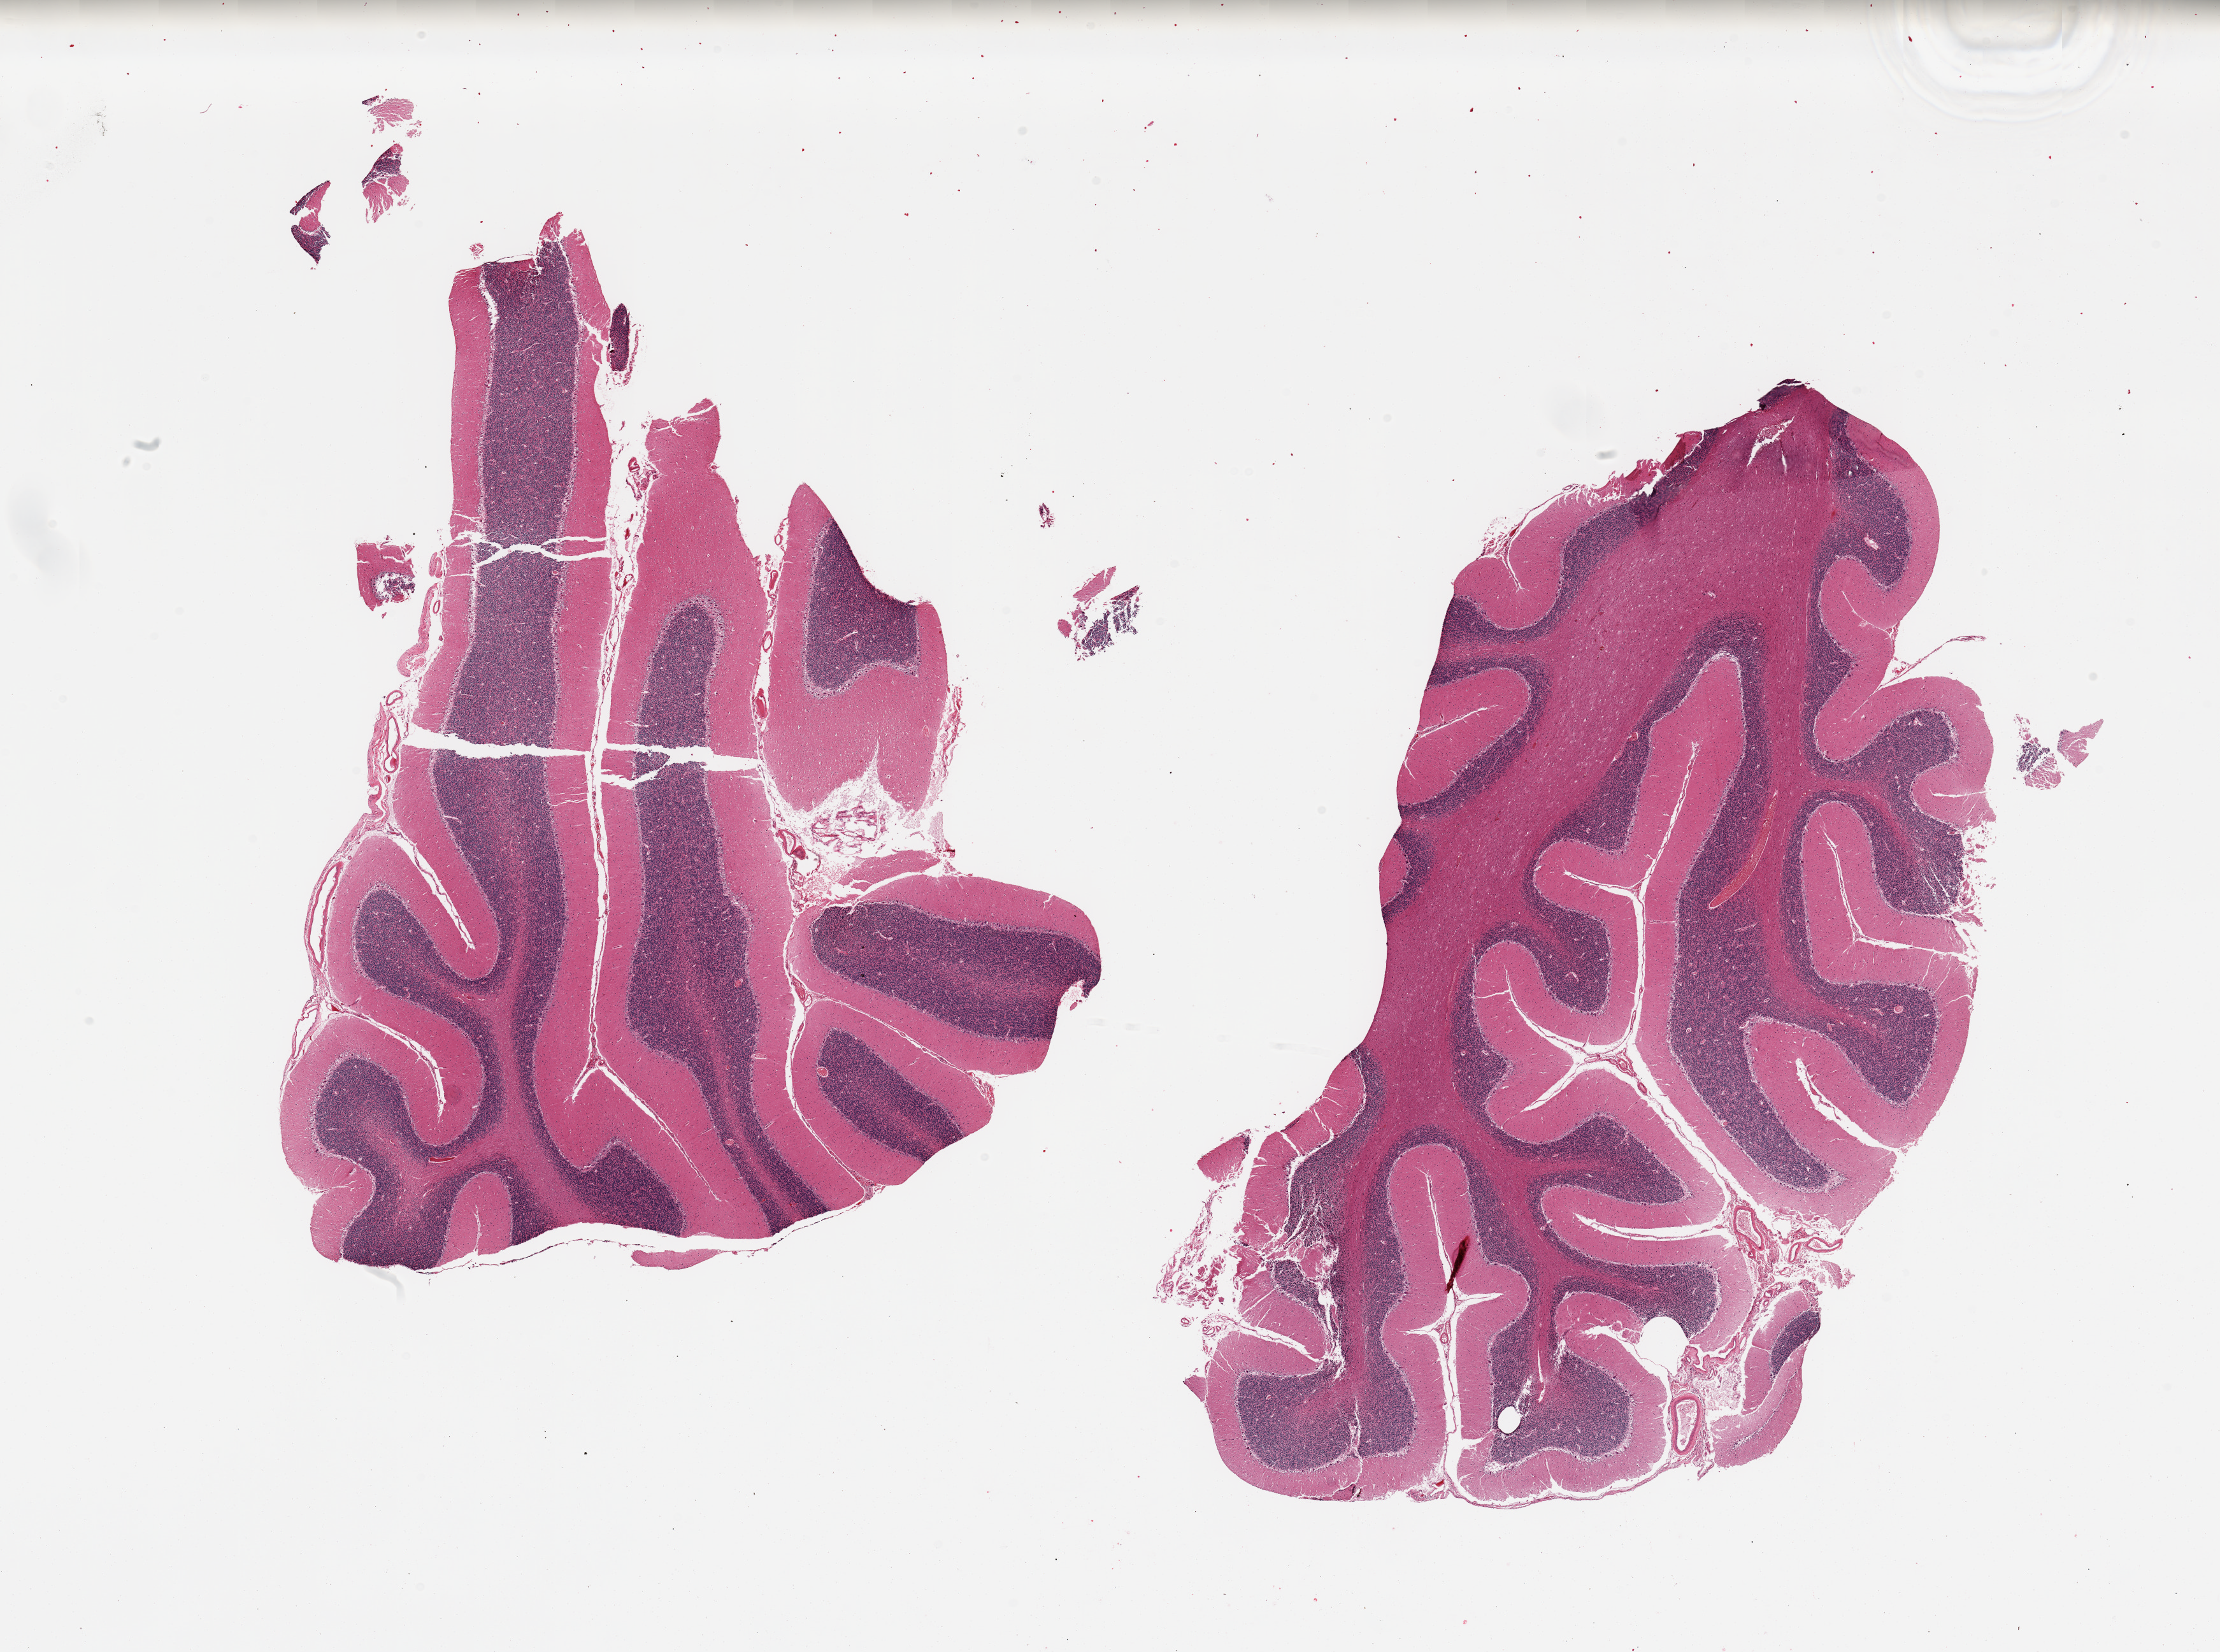
H&E whole-slide image — low-resolution overview of the scanned area, about 27.6 x 20.5 mm (from a 20x scan), PAXgene-fixed, paraffin-embedded tissue, section of cerebellum (target tissue), donor tissue sample. Donor sex: male.
Reviewer comment on this tissue sample: 2 pieces, no abnormalities.